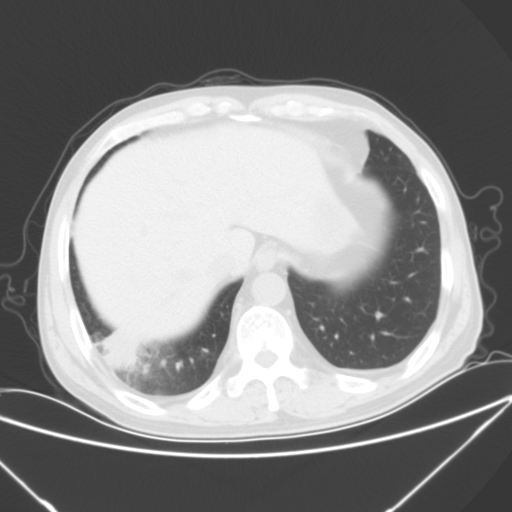
Chest CT, one axial slice; position 15 of 57 along the scan axis; 120 kVp; lung window (W 1500 / L -600 HU); 5 mm slice thickness; 512 × 512 image matrix, field of view 364 × 364 mm. Male patient, age 54 years. Case-level facts recorded for this patient, not image findings: clinical TNM (as recorded): T2 N1 M0; histopathological grade: G3.
Outlined on this slice (rectangle marked by the reading radiologist):
- lung tumour (recorded histology: adenocarcinoma): box from (x=100, y=322) to (x=139, y=368) px